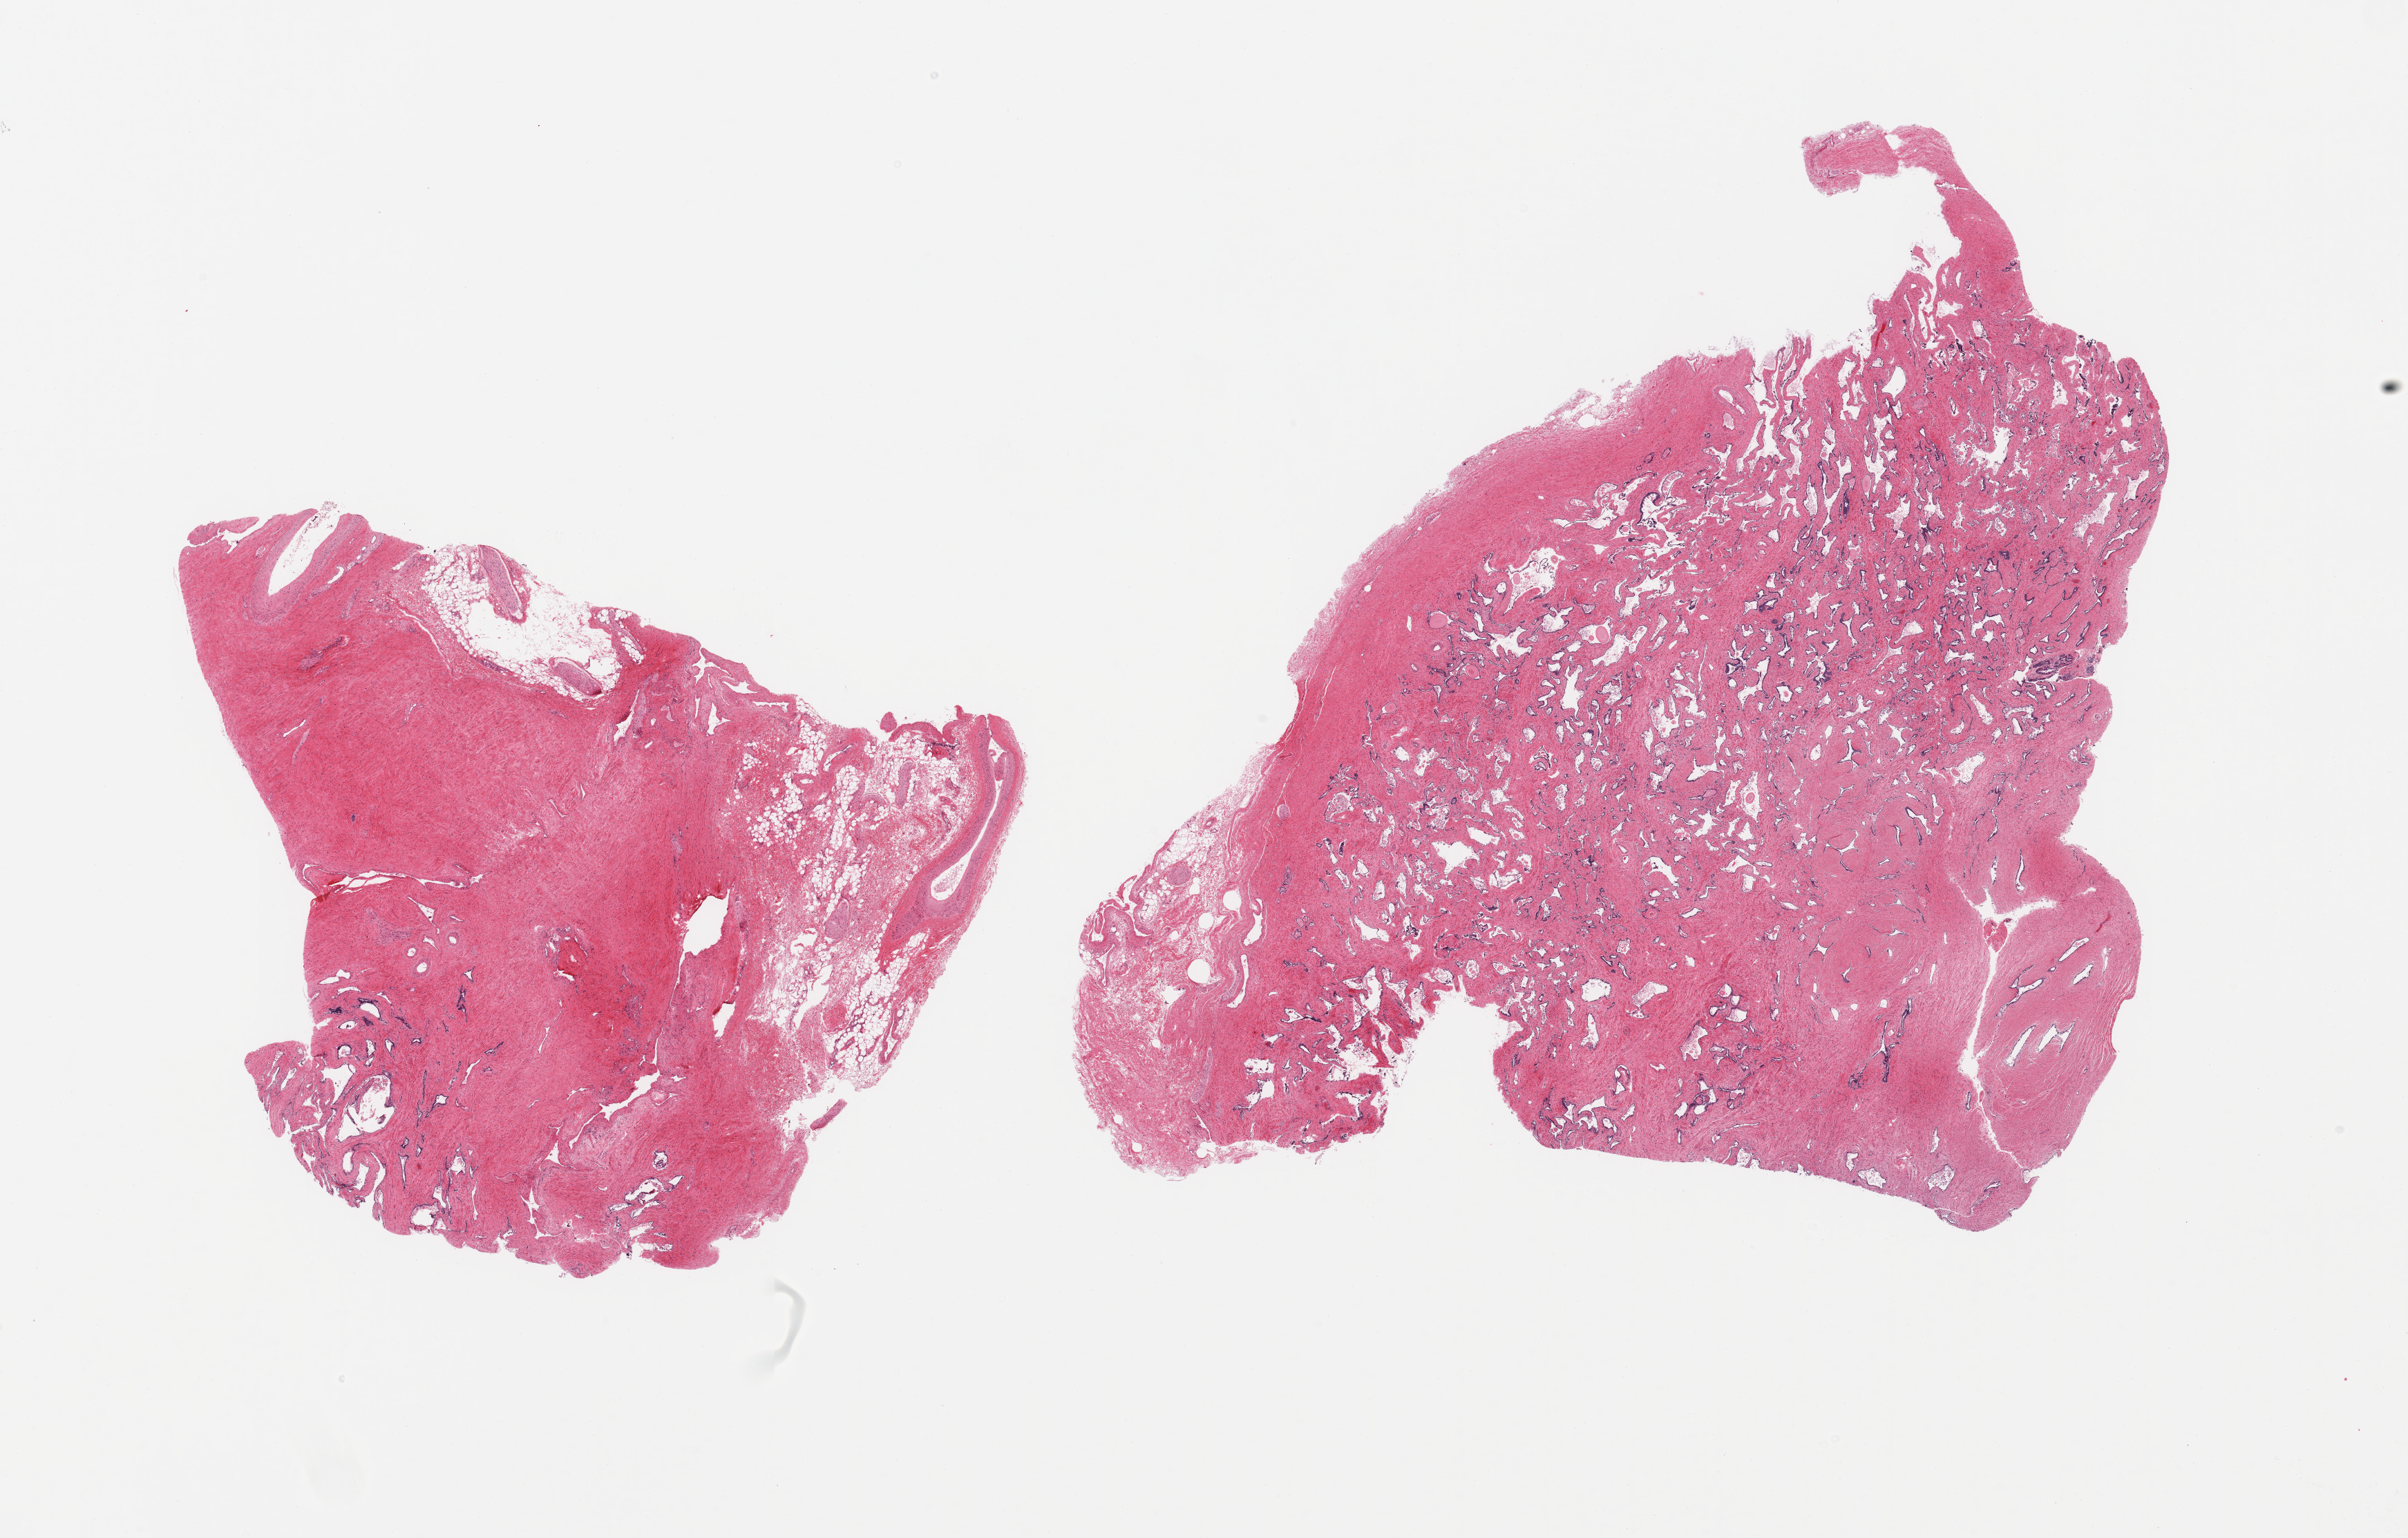
H&E whole-slide image, brightfield, shown as a low-resolution overview of the whole scanned area (about 27.6 x 17.6 mm); PAXgene-fixed, paraffin-embedded tissue; sampled site (target tissue): prostate; donor tissue sample. Male donor.
- pathologist's review note for this sample: 2 pieces atrophic glandular pattern, moderately advanced mucosal autolysis